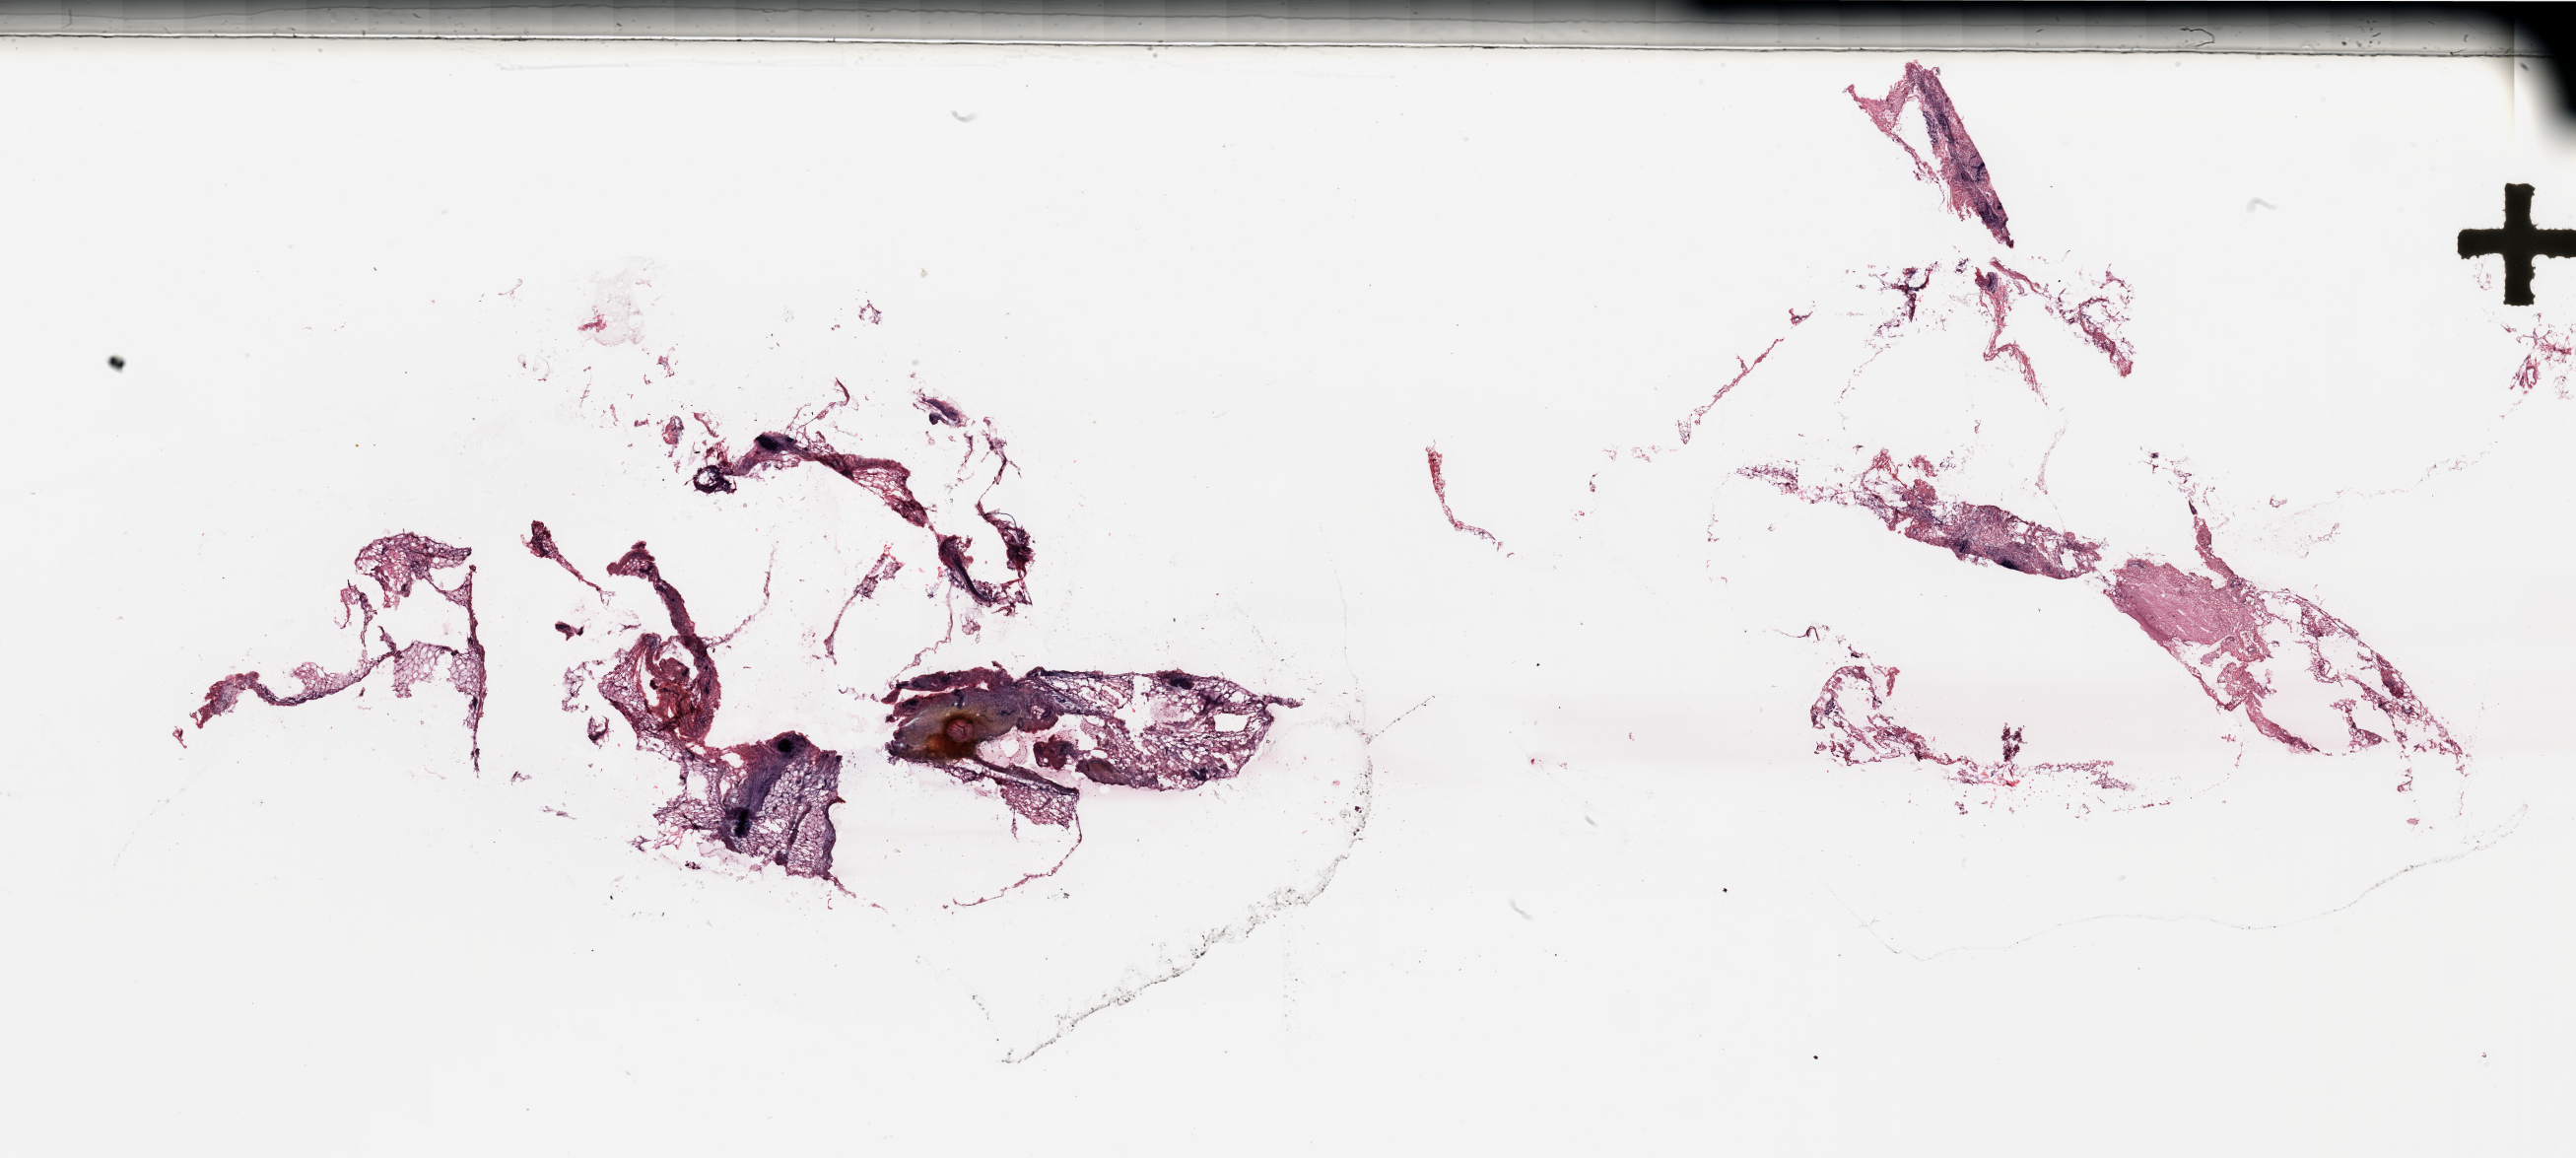
H&E-stained whole-slide image — a low-resolution overview of the entire scanned area, about 41.3 x 18.6 mm (acquisition: 20x scan), breast, tissue type not recorded.
Patient diagnosis (cohort enrolment): breast cancer (breast).